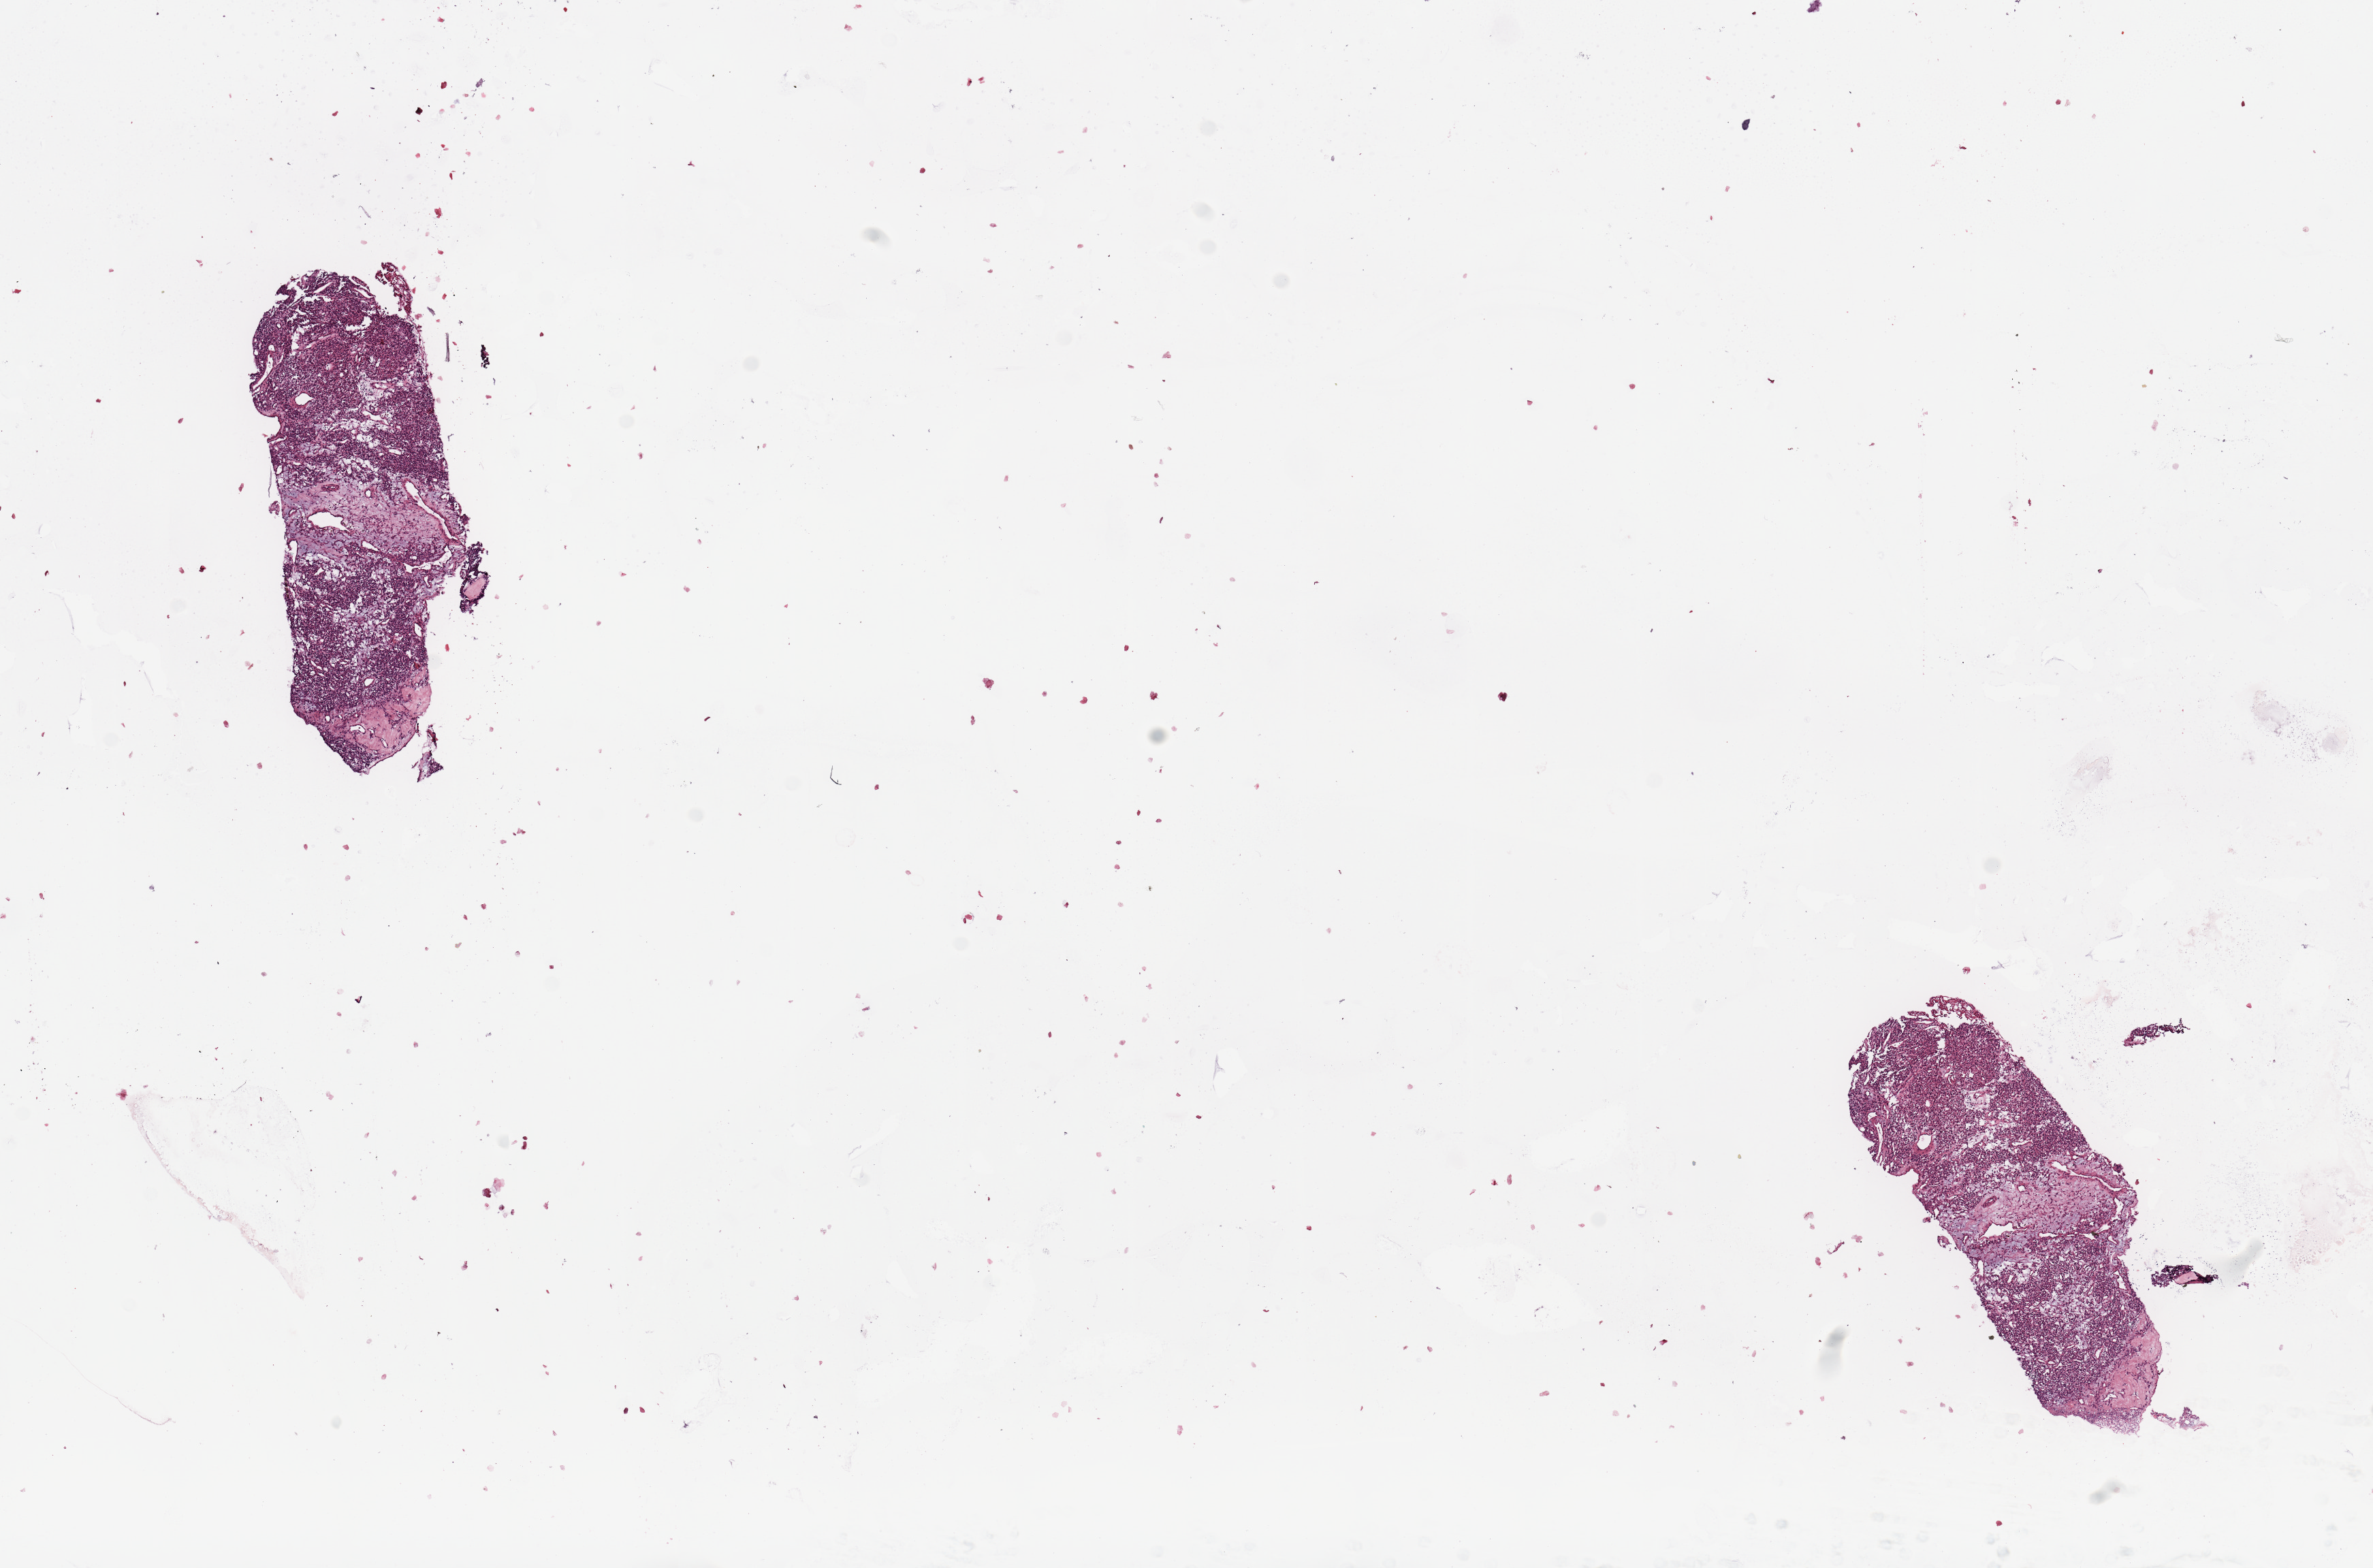
Digitized H&E tissue section (whole slide), whole scanned area (about 13.8 x 9.1 mm) shown as a low-resolution overview; kidney, tumour tissue. Patient: male, age 48 years. Histologic grade: G2 (moderately differentiated).
- primary tumour site (as recorded): middle
- histologic diagnosis: Renal cell carcinoma, NOS
- AJCC pathologic stage: I